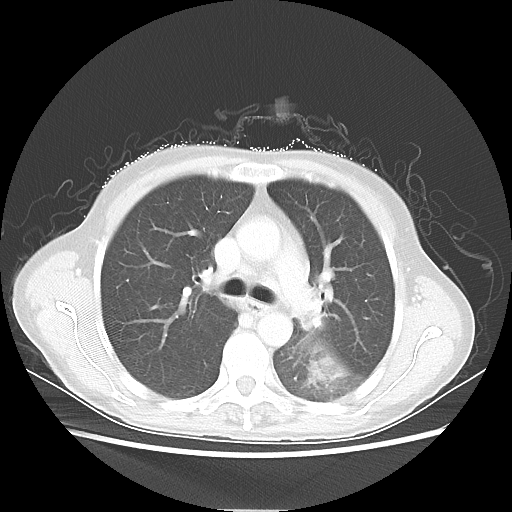
Chest CT, one axial slice. Position 36 of 56 along the scan axis. Reconstruction kernel LUNG. 80 kVp. Lung window (W 1500 / L -600 HU). 5 mm slice thickness. 512 × 512 image matrix, field of view 360 × 360 mm. Female patient, age 53 years. Case-level facts recorded for this patient, not image findings: clinical TNM (as recorded): T3 N0 M0.
Structures marked on this image (rectangle marked by the reading radiologist):
- lung tumour (recorded histology: adenocarcinoma): box from (x=301, y=341) to (x=352, y=387) px